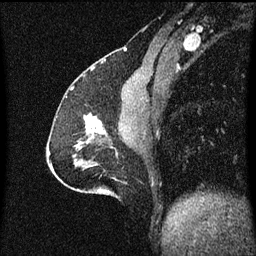
Breast MRI (dynamic contrast-enhanced), one sagittal slice. Position 25 of 60 along the scan axis. Dynamic contrast-enhanced series, image 2 of 3 at this slice position (ordered by acquisition). 1.5 T. TE 4.2 ms, TR 8.4 ms. 2 mm slice thickness. 256 × 256 image matrix, field of view 200 × 200 mm. Female patient, age 51 years.
Structures marked on this image (semi-automatic segmentation, software-assisted and operator-edited):
- analysis volume of interest (the breast-tissue region the enhancement analysis was run in; not a lesion): bounding box (x1, y1, x2, y2) in pixels: (84, 114, 107, 139)
- tumour enhancement mask (voxels above the 70 % enhancement threshold inside the analysis volume of interest): (84, 114, 103, 133)